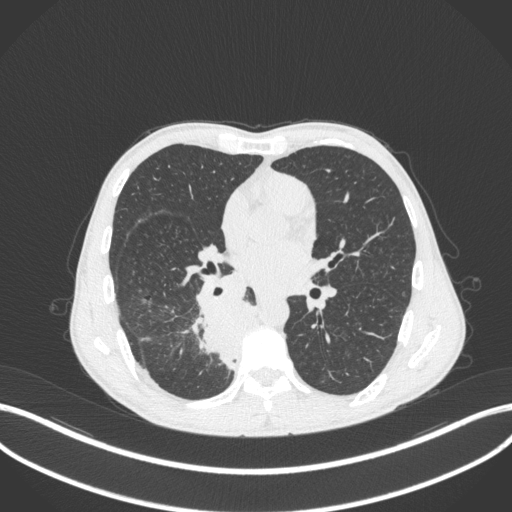
Chest CT, one axial slice. Slice 188 of 371 in the series (ordered by position). Reconstruction kernel B31f. Lung window (W 1500 / L -600 HU). 1 mm slice thickness. 512 × 512 image matrix, field of view 400 × 400 mm. Male patient, age 58 years. Case-level facts recorded for this patient, not image findings: clinical TNM (as recorded): T3 N1 M1.
Annotated regions visible in this slice (rectangle marked by the reading radiologist):
- lung tumour (recorded histology: squamous cell carcinoma): bounding box (x1, y1, x2, y2) in pixels: (195, 296, 269, 373)